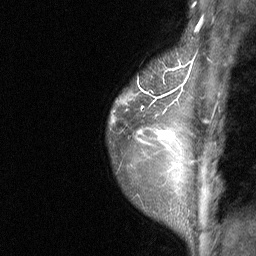
Breast MRI (dynamic contrast-enhanced), one sagittal slice. Slice 53 of 64 in the series (ordered by position). Dynamic contrast-enhanced study with each time point stored as its own series, time point 2 of 3 at this slice position (early post-contrast, ordered by acquisition time). 1.5 T. TE 4.8 ms, TR 27 ms. 256 × 256 image matrix. Female patient, age 34 years. Case-level facts recorded for this patient, not image findings: setting: breast cancer imaged before/during neoadjuvant chemotherapy; receptor status: HR-positive, HER2-negative.
Annotated regions visible in this slice (semi-automatic segmentation, software-assisted and operator-edited):
- analysis volume of interest (the breast-tissue region the enhancement analysis was run in; not a lesion): bounding box (x1, y1, x2, y2) in pixels: (106, 45, 181, 191)
- tumour enhancement mask (voxels above the 90 % enhancement threshold inside the analysis volume of interest): (142, 96, 172, 138)